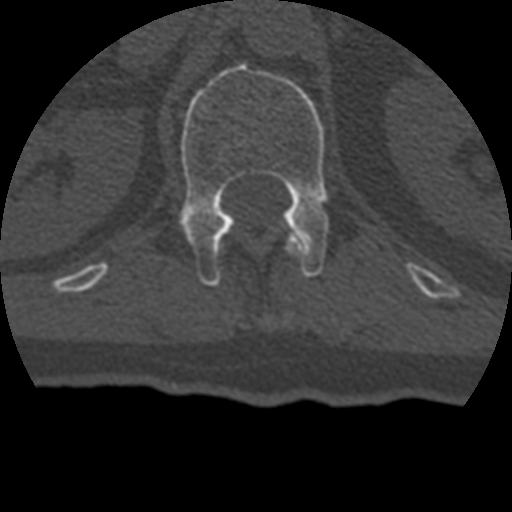
CT including the spine, one axial slice. Slice 154 of 399 in the series (ordered by position). 120 kVp. Bone window (W 1800 / L 400 HU). 1.25 mm slice thickness. 512 × 512 image matrix. Patient age 69 years. From the clinical record (not read from this slice): primary cancer: prostate.
Structures marked on this image (semi-automatic segmentation, software-assisted and operator-edited):
- L1 vertebra: bounding box (x1, y1, x2, y2) in pixels: (179, 63, 329, 286)
- T12 vertebra: (286, 234, 305, 255)